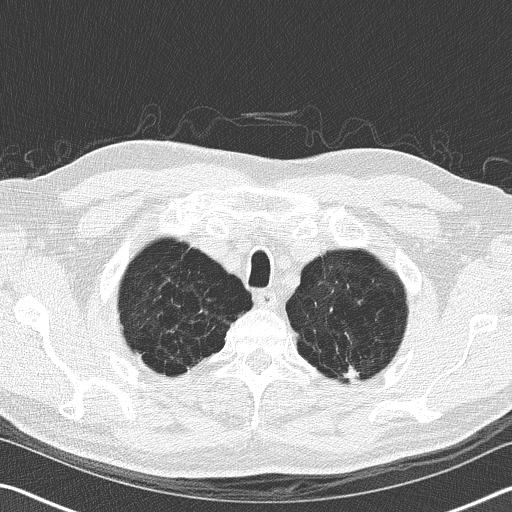
Chest CT (low-dose screening protocol), one axial image. First (baseline) screen. Lung window (W 1500 / L -600 HU). 2 mm slice thickness. Lung (sharp) reconstruction kernel (B50f). Slice 22 of 167 in the series. 512 × 512 image matrix, field of view 340 × 340 mm. Male, age 62 years at enrolment. Former smoker at enrolment.
• Expert-annotated lung lesion, bounding box [x1, y1, x2, y2] px = [332, 350, 376, 397].
• Reader record for this screening exam (exam-level; its link to the box is not recorded): non-calcified nodule or mass ≥4 mm, left upper lobe, 10 × 10 mm.
• Lung cancer was diagnosed 561 days after this screen: adenocarcinoma, NOS, left upper lobe, moderately differentiated (G2), stage IA (AJCC 6th edition), 10 mm at pathology.